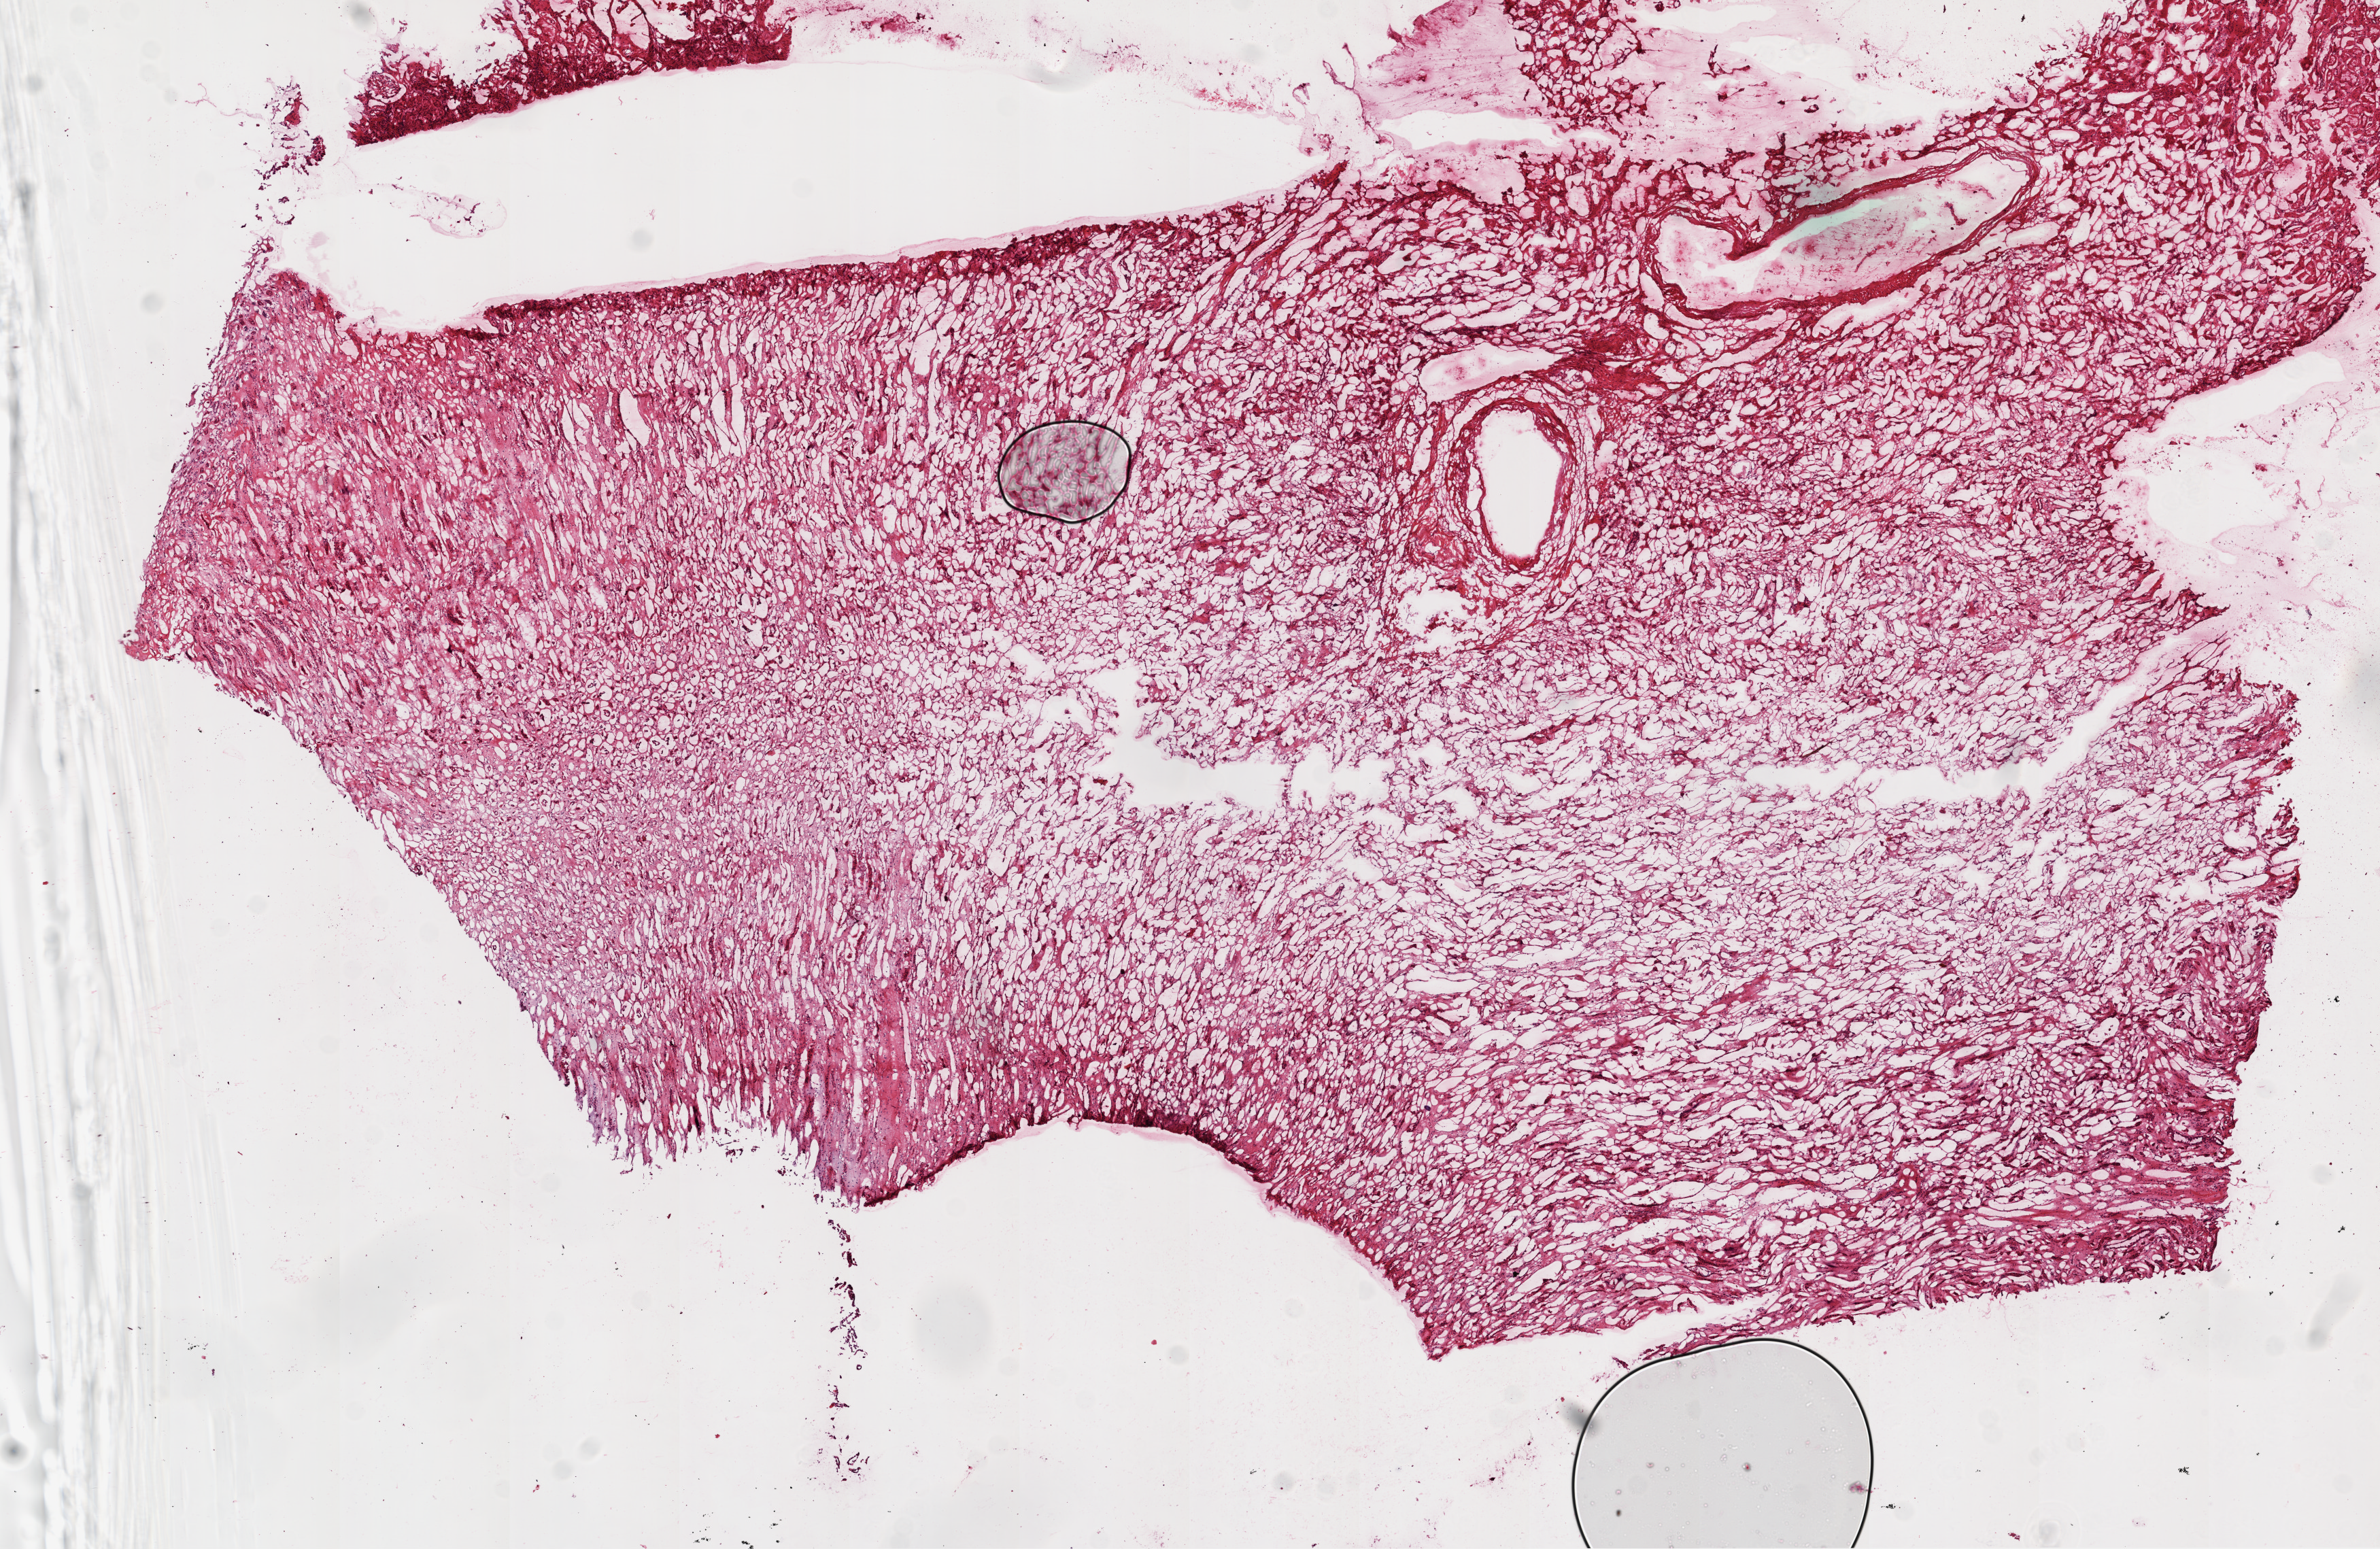
Whole-slide histology image, Hematoxylin and eosin (H&E) stained — a low-resolution overview of the entire scanned area, about 14.0 x 9.1 mm; frozen section; sample: solid tissue normal (non-tumour tissue), kidney. Patient: female, age at initial diagnosis 77 years.
This section: solid tissue normal (non-tumour) sample from the same patient. Patient diagnosis: Clear cell adenocarcinoma, NOS.